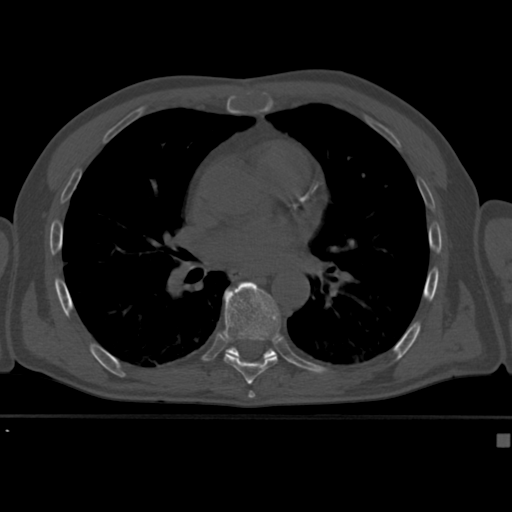
CT including the spine, one axial slice; 120 kVp; bone window (W 1800 / L 400 HU); 1.5 mm slice thickness; 512 × 512 image matrix. Male patient, age 64 years. Case-level facts recorded for this patient, not image findings: primary cancer: uterus; vertebrae with lytic lesions (as recorded): T1, T4, T5, T7, L5.
Outlined on this slice (semi-automatic segmentation, software-assisted and operator-edited):
- T8 vertebra: bounding box [x1, y1, x2, y2] px = [223, 281, 280, 382]
- T9 vertebra: [225, 347, 280, 361]